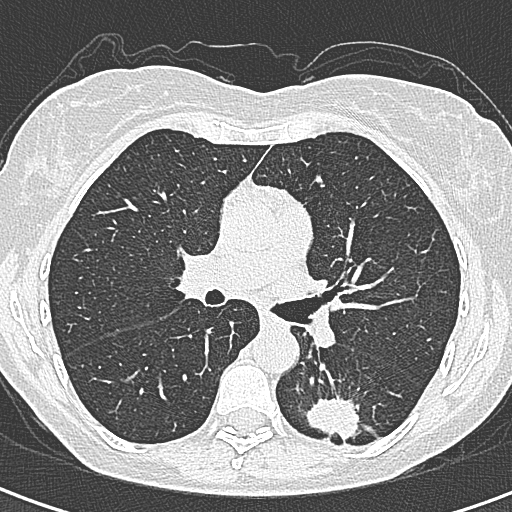
Axial slice from a low-dose chest CT screening exam. First (baseline) screen. Lung window (W 1500 / L -600 HU). 1 mm slice thickness. Lung (sharp) reconstruction kernel (B80f). Female participant, aged 58 years at enrolment.
• Lesion marked by an expert reader, bounding box (x1, y1, x2, y2) in pixels: (295, 388, 365, 456).
• The screening reader recorded 2 non-calcified nodules or masses ≥4 mm on this exam (left lower lobe, right lower lobe); which of them this box marks is not recorded.
• Official screen result: positive, change unspecified: nodule(s) >= 4 mm or enlarging nodule(s), mass(es), or other non-specific abnormalities suspicious for lung cancer.